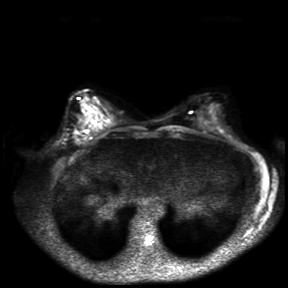
Breast MRI, one axial slice; slice 16 of 30 in the series (ordered by position); diffusion-weighted series; image 2 of 4 stored at this slice position (different b-values; order by instance number); 3 T; 4 mm slice thickness; 288 × 288 image matrix, field of view 360 × 360 mm. Female patient.
Structures marked on this image (manually delineated by an expert):
- tumour on diffusion-weighted imaging: bounding box [x1, y1, x2, y2] px = [80, 135, 89, 141]